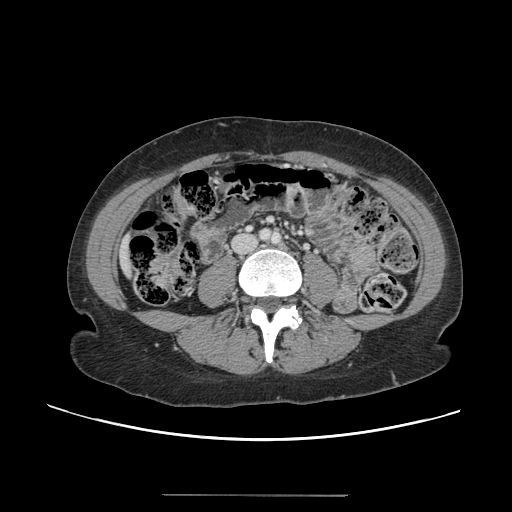
Contrast-enhanced abdominal CT, one axial slice; slice 13 of 144 in the series (ordered by position); 120 kVp; intravenous contrast given; soft-tissue window (W 400 / L 40 HU); 2.5 mm slice thickness; 512 × 512 image matrix. Female patient, age 53 years. From the clinical record (not read from this slice): diagnosis: colorectal cancer liver metastases, imaged before liver resection; multiple liver metastases: yes; largest metastasis: 1.1 cm; disease in both lobes: no.
Outlined on this slice (outlined manually by an expert reader):
- liver: bounding box <121,240,131,275> (left, top, right, bottom; pixels)
- planned liver remnant (the part of the liver to remain after resection): <122,241,131,275>